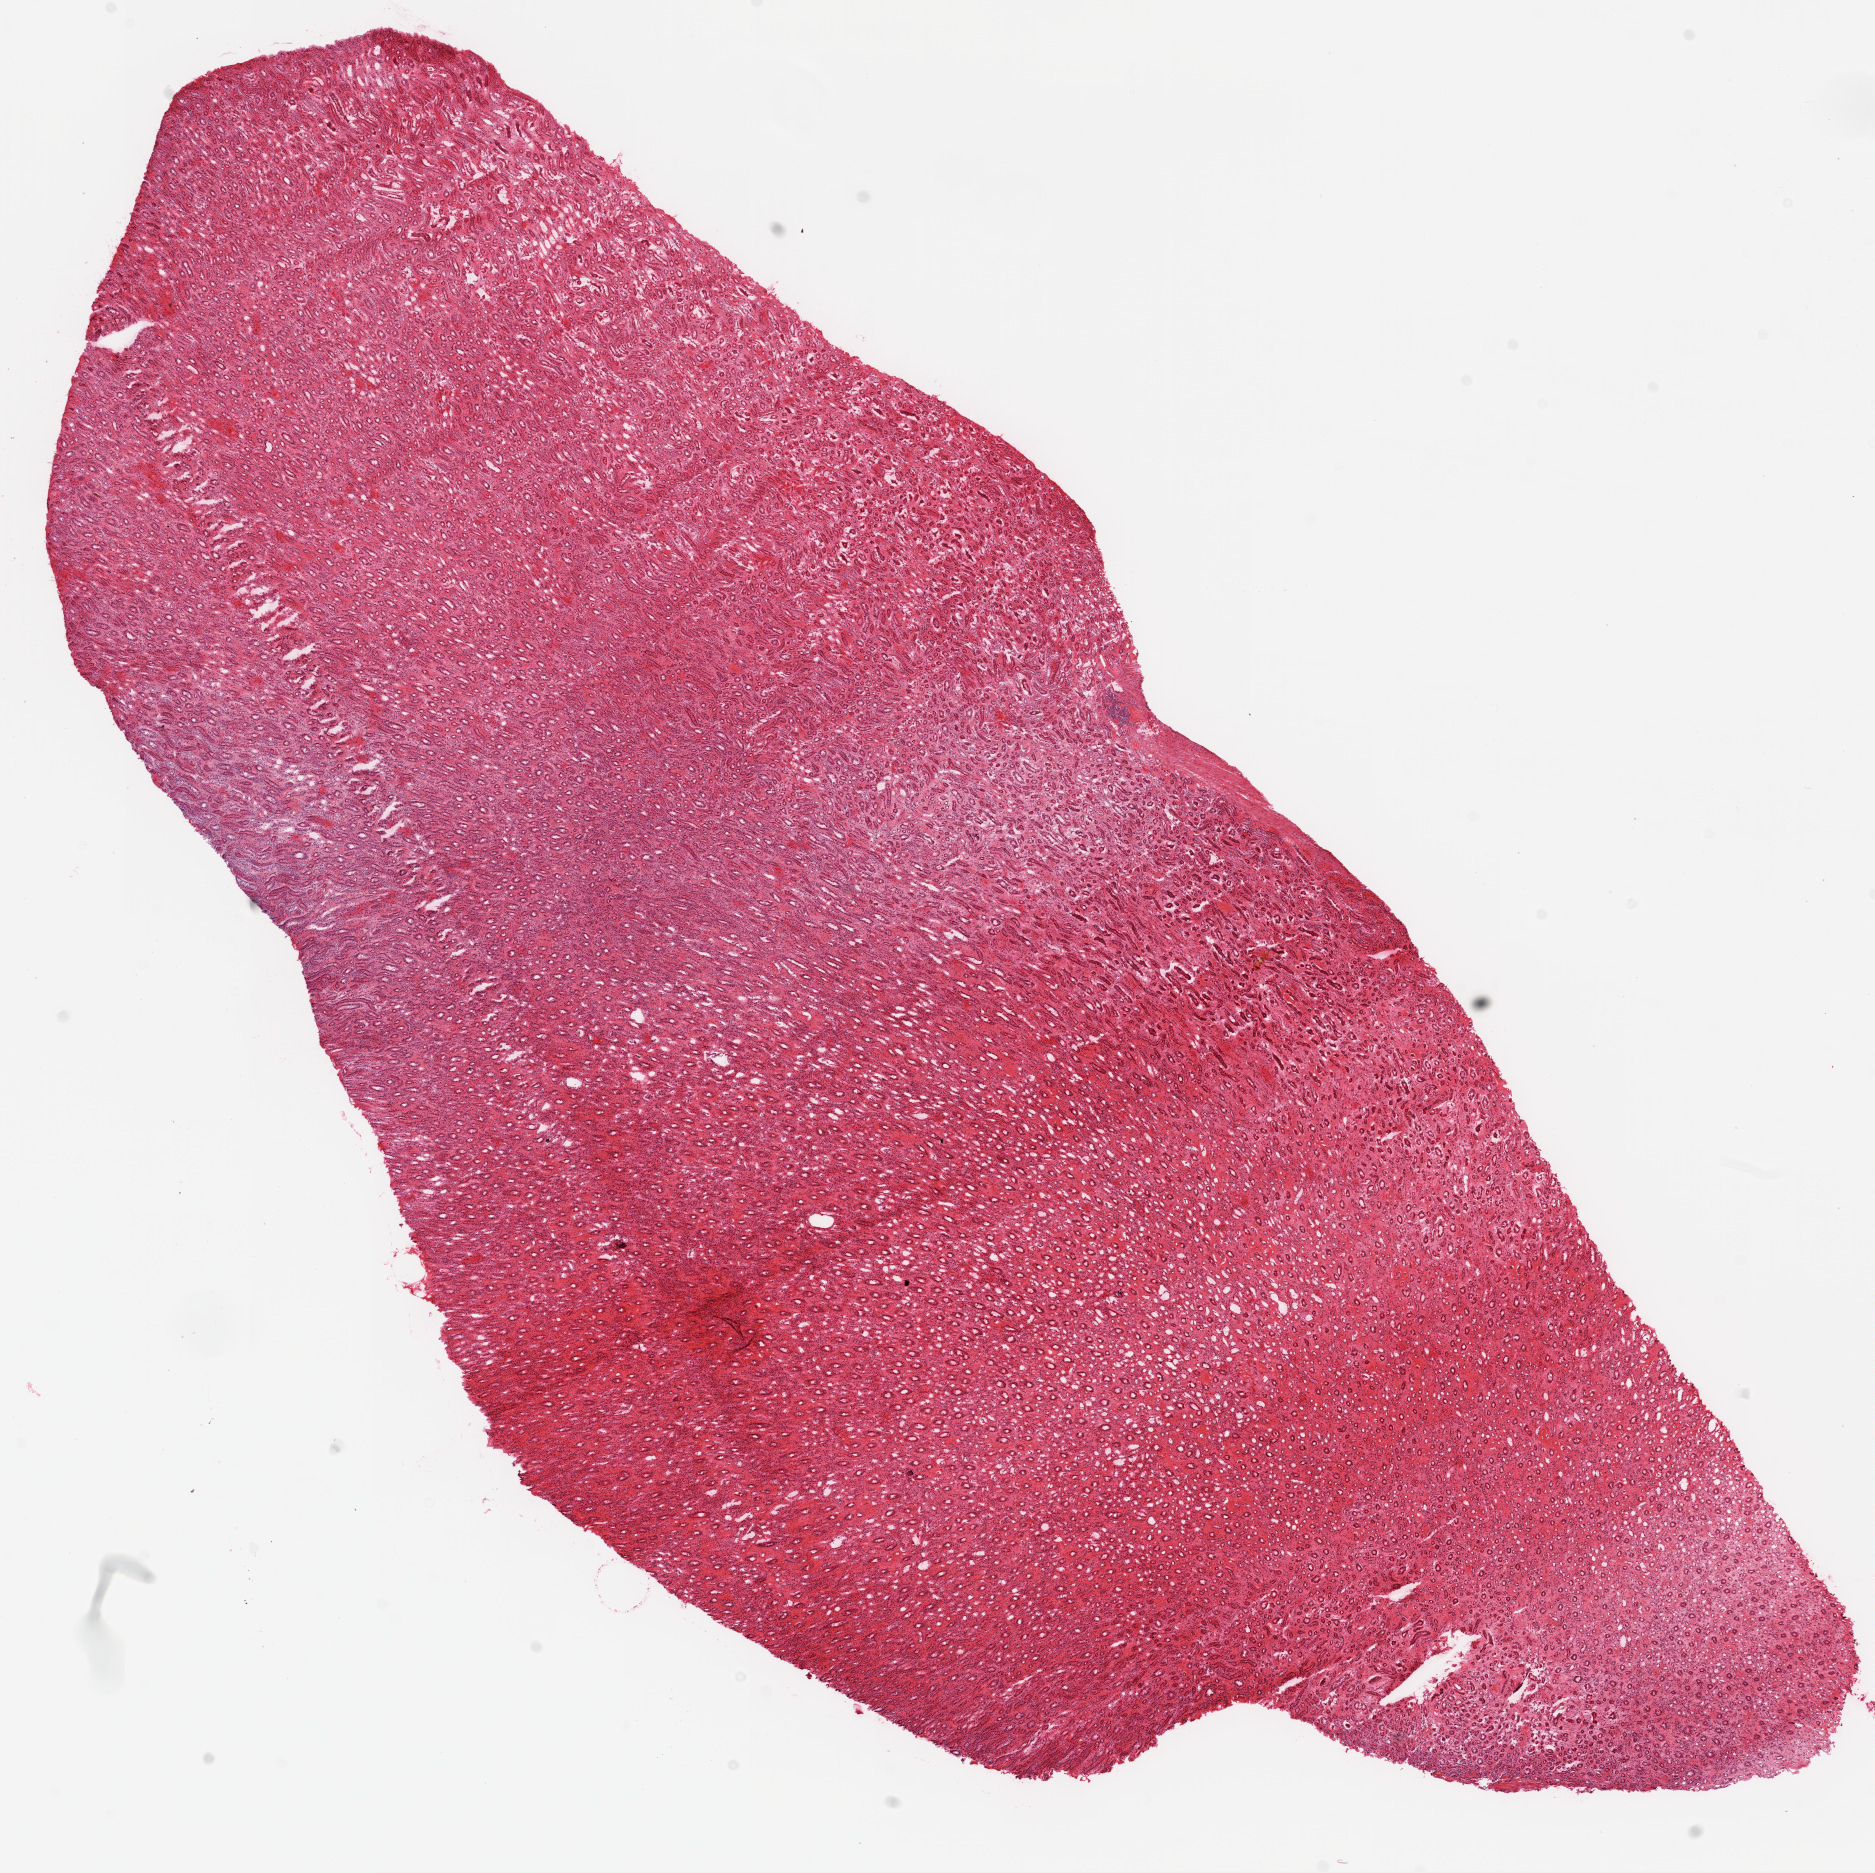
Digitized H&E-stained tissue section (whole slide) — a low-resolution overview of the entire scanned area, about 15.0 x 15.0 mm (slide scanned at 20x); frozen section from the top of the tissue portion; solid tissue normal (non-tumour tissue) sample from the kidney. Male, age 41 years at initial diagnosis.
This section: solid tissue normal (non-tumour) sample from the same patient. Patient diagnosis: Clear cell adenocarcinoma, NOS.